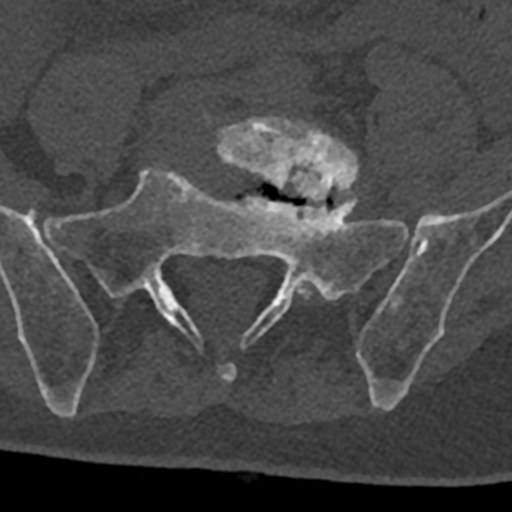
CT including the spine, one axial slice. Slice 159 of 797 in the series (ordered by position). Reconstruction kernel Br40s/3. 120 kVp. Bone window (W 1800 / L 400 HU). 0.5 mm slice thickness. 512 × 512 image matrix. Patient: male, 74 years. Case-level facts recorded for this patient, not image findings: primary cancer: renal; vertebrae with lytic lesions (as recorded): T10, L1, L2, L3, L4, L5.
Annotated regions visible in this slice (semi-automatic segmentation, software-assisted and operator-edited):
- L5 vertebra: box from (x=215, y=116) to (x=359, y=299) px